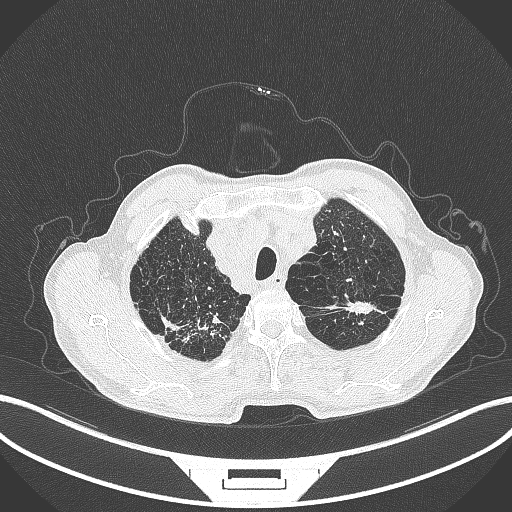
Chest CT, one axial slice; position 380 of 463 along the scan axis; reconstruction kernel B70f; 120 kVp; lung window (W 1500 / L -600 HU); 1 mm slice thickness; 512 × 512 image matrix. Patient: male, 74 years. Case-level facts recorded for this patient, not image findings: clinical TNM (as recorded): T2a N1 M0.
Annotated regions visible in this slice (rectangle marked by the reading radiologist):
- lung tumour (recorded histology: adenocarcinoma): bounding box [x1, y1, x2, y2] px = [328, 293, 373, 317]